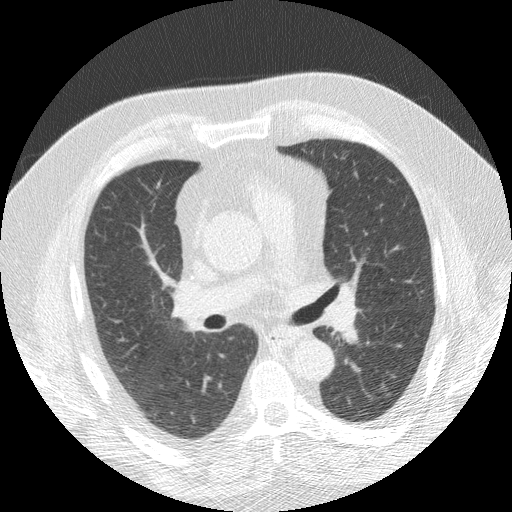
Axial slice from a low-dose chest CT screening exam. Baseline screening round. Lung window (W 1500 / L -600 HU). Slice 68 of 166 in the series. Male participant, aged 69 years at enrolment. Former smoker at enrolment.
Expert reader's lesion annotation, bounding box [x1, y1, x2, y2] px = [364, 378, 402, 417]. Screening reader's record for this exam: no non-calcified nodule ≥4 mm recorded. Later outcome: lung cancer diagnosed 939 days after this screen — squamous cell carcinoma, NOS, left lower lobe, moderately differentiated (G2), stage IA (AJCC 6th edition), 14 mm at pathology.